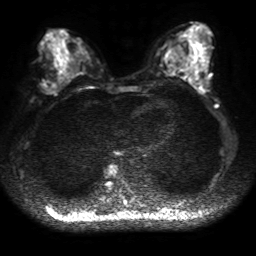
Breast MRI, one axial slice. Position 22 of 50 along the scan axis. Diffusion-weighted series; image 2 of 4 stored at this slice position (different b-values; order by instance number). 1.5 T. 4 mm slice thickness. 256 × 256 image matrix, field of view 320 × 320 mm. Female patient.
Structures marked on this image (outlined manually by an expert reader):
- tumour on diffusion-weighted imaging: bounding box (x1, y1, x2, y2) in pixels: (41, 81, 57, 94)